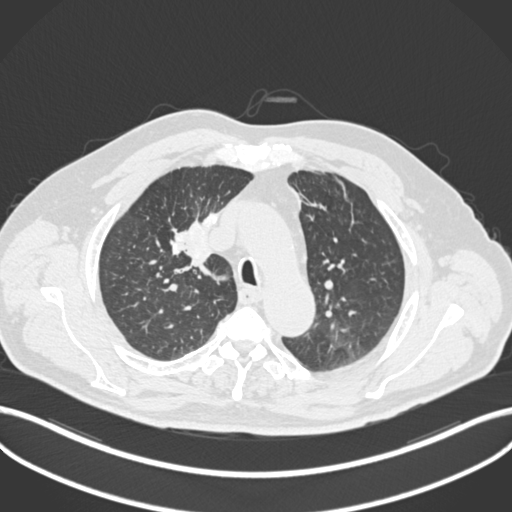
Chest CT, one axial slice. Position 147 of 255 along the scan axis. 120 kVp. Lung window (W 1500 / L -600 HU). 1 mm slice thickness. 512 × 512 image matrix. Patient: male, 60 years. Case-level facts recorded for this patient, not image findings: clinical TNM (as recorded): T1b N1 M0.
Annotated regions visible in this slice (rectangle marked by the reading radiologist):
- lung tumour (recorded histology: squamous cell carcinoma): bounding box [x1, y1, x2, y2] px = [163, 213, 226, 278]